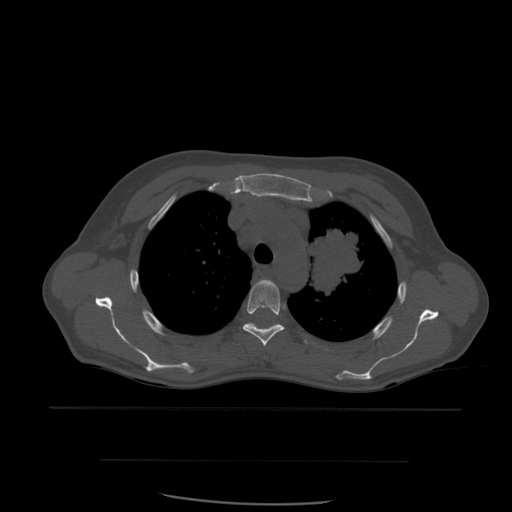
CT including the spine, one axial slice. Slice 426 of 574 in the series (ordered by position). Bone window (W 1800 / L 400 HU). 1.25 mm slice thickness. 512 × 512 image matrix, field of view 392 × 392 mm. Patient age 48 years. From the clinical record (not read from this slice): primary cancer: lung; vertebrae with lytic lesions (as recorded): T11.
Annotated regions visible in this slice (semi-automatic segmentation, software-assisted and operator-edited):
- T4 vertebra: bounding box [x1, y1, x2, y2] px = [243, 279, 285, 347]
- T5 vertebra: [247, 323, 276, 326]